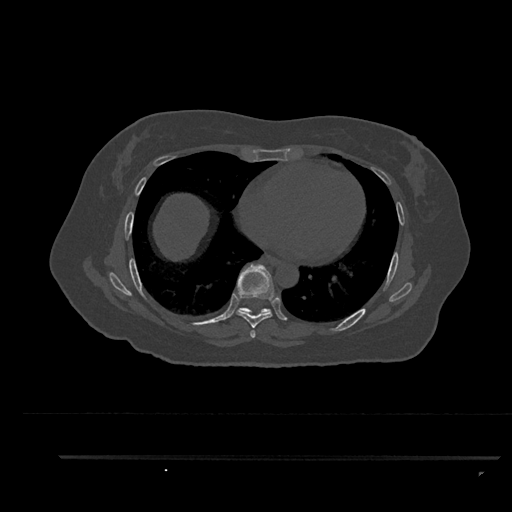
CT including the spine, one axial slice; position 495 of 797 along the scan axis; reconstruction kernel Br40s/3; 120 kVp; bone window (W 1800 / L 400 HU); 0.5 mm slice thickness; 512 × 512 image matrix, field of view 408 × 408 mm. Female patient, age 44 years. From the clinical record (not read from this slice): primary cancer: renal; vertebrae with lytic lesions (as recorded): L1.
Outlined on this slice (semi-automatically segmented with operator editing):
- T6 vertebra: bounding box <252,334,255,337> (left, top, right, bottom; pixels)
- T7 vertebra: <236,264,275,338>
- T8 vertebra: <236,308,271,315>